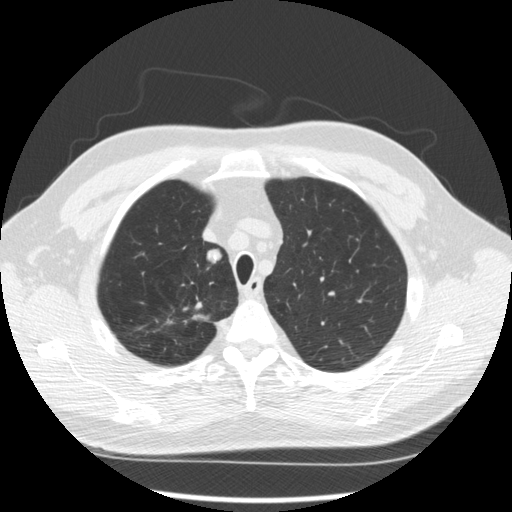
Low-dose screening chest CT, axial slice. Second screening round (one year after baseline). Lung window (W 1500 / L -600 HU). 512 × 512 image matrix. Male, age 64 years at enrolment. Former smoker at enrolment.
2 expert-annotated lung lesions on this slice (largest first), bounding box (x1, y1, x2, y2) in pixels: (169, 297, 221, 332); (189, 245, 226, 272). The screening reader recorded 3 non-calcified nodules or masses ≥4 mm on this exam (right upper lobe, right upper lobe, right upper lobe); which of them these boxes mark is not recorded. Later outcome: lung cancer diagnosed 411 days after this screen (after the third annual screen) — adenocarcinoma, NOS, right upper lobe, moderately differentiated (G2), stage IA (AJCC 6th edition), 14 mm at pathology.